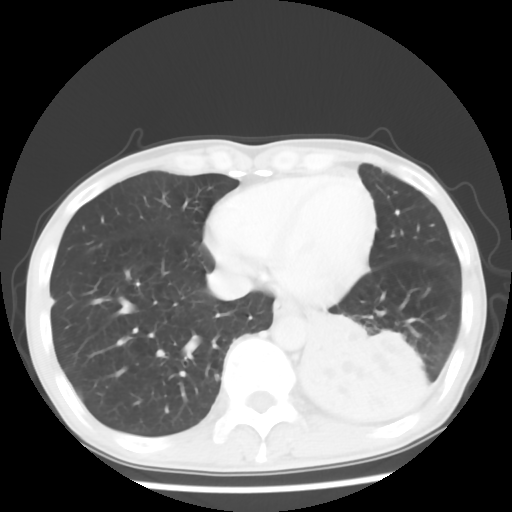
Chest CT, one axial slice. Position 17 of 64 along the scan axis. 120 kVp. Lung window (W 1500 / L -600 HU). 512 × 512 image matrix, field of view 313 × 313 mm. Patient: male, 68 years. From the clinical record (not read from this slice): clinical TNM (as recorded): T4 N0 M0.
Annotated regions visible in this slice (rectangle marked by the reading radiologist):
- lung tumour (recorded histology: squamous cell carcinoma): bounding box <295,307,437,434> (left, top, right, bottom; pixels)